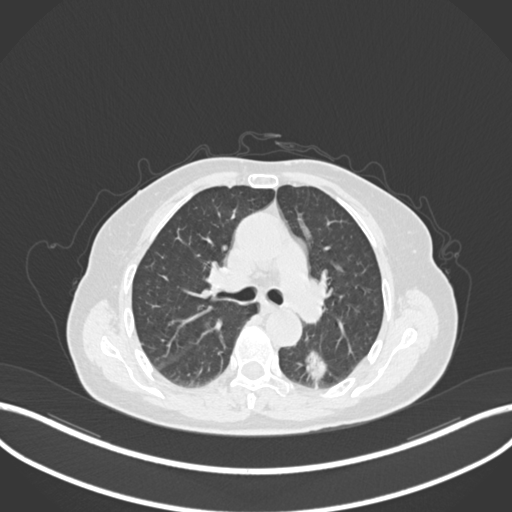
Chest CT, one axial slice; position 533 of 727 along the scan axis; reconstruction kernel B30f; lung window (W 1500 / L -600 HU); 1 mm slice thickness; 512 × 512 image matrix. Female patient, age 70 years. From the clinical record (not read from this slice): clinical TNM (as recorded): T1c N0 M0.
Annotated regions visible in this slice (rectangle marked by the reading radiologist):
- lung tumour (recorded histology: adenocarcinoma): bounding box [x1, y1, x2, y2] px = [299, 348, 331, 384]